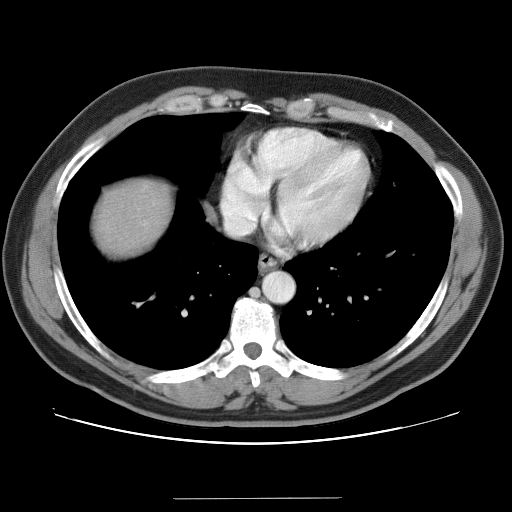
Contrast-enhanced abdominal CT (liver protocol), one axial slice. Position 37 of 40 along the scan axis. 120 kVp. Soft-tissue window (W 400 / L 40 HU). 512 × 512 image matrix, field of view 380 × 380 mm. Case-level facts recorded for this patient, not image findings: diagnosis: hepatocellular carcinoma (patient treated with transarterial chemoembolisation; whether this scan precedes or follows treatment is not stated here); TNM stage (as recorded): Stage-IVA; Child-Pugh class: B; tumour nodularity: multinodular.
Outlined on this slice (semi-automatically segmented with operator editing):
- liver parenchyma outside the tumour (the mass and vessels are separate outlines, so this box may not span the whole liver): bounding box <96,180,170,254> (left, top, right, bottom; pixels)